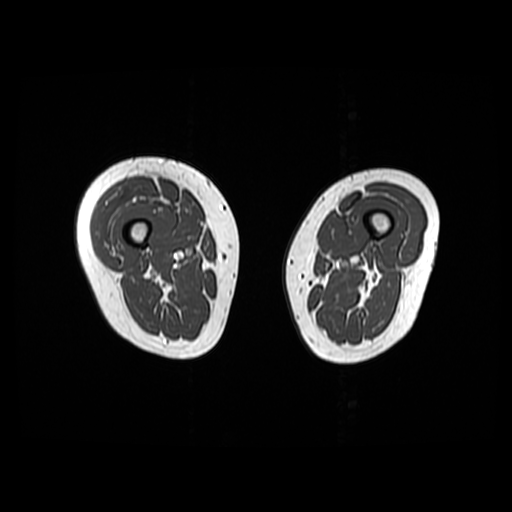
MRI of an extremity soft-tissue mass, one axial slice. Position 14 of 48 along the scan axis. 6 mm slice thickness. 512 × 512 image matrix, field of view 440 × 440 mm. Female patient. Case-level facts recorded for this patient, not image findings: histological type: pleiomorphic undifferentiated sarcoma; grade: high; site of the primary tumour: right quadricep.
Outlined on this slice (outlined manually by an expert reader):
- gross tumour volume including surrounding oedema: bounding box (x1, y1, x2, y2) in pixels: (92, 177, 155, 248)